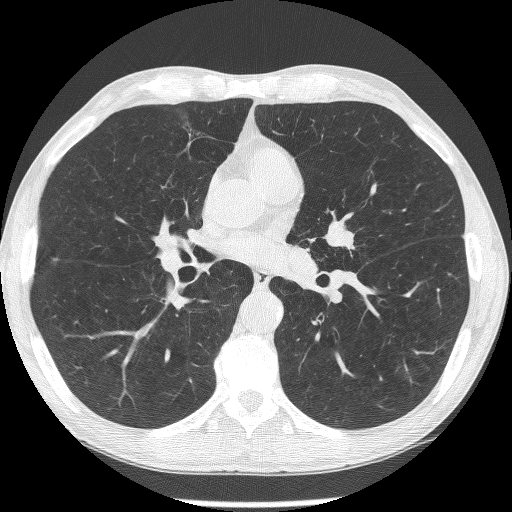
Chest CT (low-dose screening protocol), one axial image; second annual screen; lung window (W 1500 / L -600 HU); 1.25 mm slice thickness; lung (sharp) reconstruction kernel (BONE); slice 141 of 293 in the series. Male, age 62 years at enrolment. Former smoker at enrolment.
Lesion marked by an expert reader, box from (x=319, y=217) to (x=368, y=265) px. The screening reader recorded 2 non-calcified nodules or masses ≥4 mm on this exam (lingula, lingula); which of them this box marks is not recorded. Participant outcome: lung cancer diagnosed 95 days after this screen — small cell carcinoma, NOS, left upper lobe, stage IIIA (AJCC 6th edition).